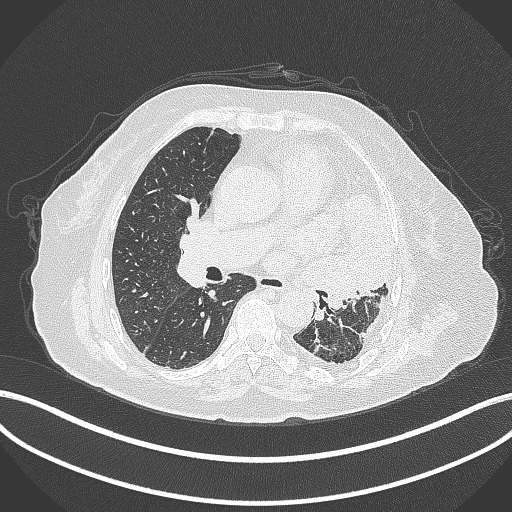
Chest CT, one axial slice; position 198 of 399 along the scan axis; reconstruction kernel B70f; 120 kVp; lung window (W 1500 / L -600 HU); 1 mm slice thickness; 512 × 512 image matrix, field of view 400 × 400 mm. Patient: female, 75 years. Case-level facts recorded for this patient, not image findings: clinical TNM (as recorded): T3 N3 M1.
Annotated regions visible in this slice (rectangle marked by the reading radiologist):
- lung tumour (recorded histology: adenocarcinoma): bounding box <306,190,397,309> (left, top, right, bottom; pixels)